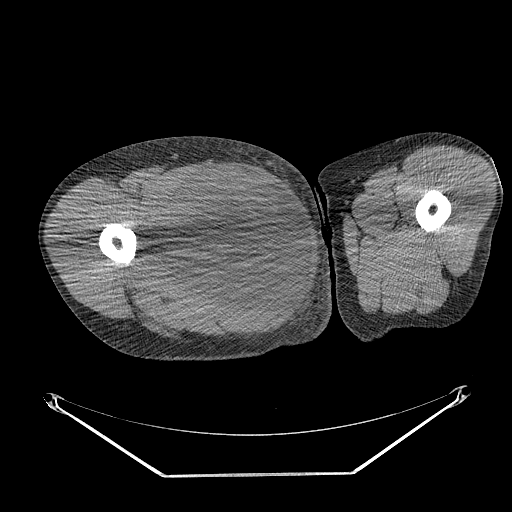
CT of an extremity soft-tissue mass (from a PET/CT study), one axial slice. Position 261 of 311 along the scan axis. 140 kVp. Soft-tissue window (W 400 / L 40 HU). 3.75 mm slice thickness. 512 × 512 image matrix, field of view 500 × 500 mm. Male patient. Case-level facts recorded for this patient, not image findings: histological type: undifferentiated - pleiomorphic; grade: high; site of the primary tumour: right thigh.
Annotated regions visible in this slice (expert contour drawn on MRI and transferred to this co-registered scan by the dataset authors):
- gross tumour volume including surrounding oedema: box from (x=144, y=167) to (x=268, y=280) px
- gross tumour volume (mass): (x=153, y=169)–(x=268, y=277)